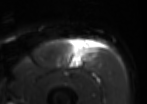
MRI of an extremity soft-tissue mass, one axial slice. Slice 37 of 85 in the series (ordered by position). T2-weighted fat-saturated. MR volume resampled by the dataset authors to the PET/CT grid (not the native acquisition matrix). 3.27 mm slice thickness. 147 × 104 image matrix. Male patient. Case-level facts recorded for this patient, not image findings: histological type: extraskeletal osteosarcoma; grade: high; site of the primary tumour: thigh.
Outlined on this slice (expert contour drawn on MRI and transferred to this co-registered scan by the dataset authors):
- gross tumour volume (mass): box from (x=67, y=42) to (x=88, y=68) px